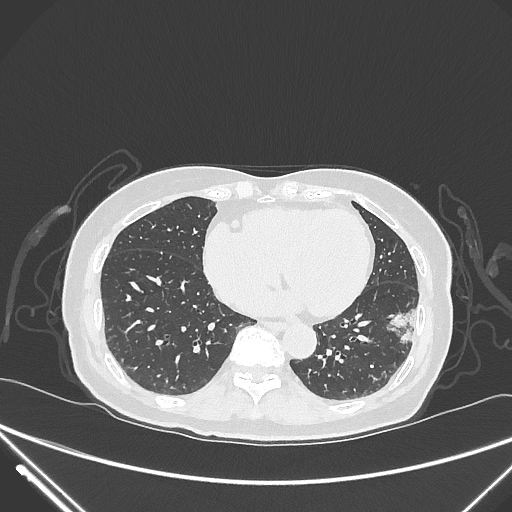
Chest CT, one axial slice. Slice 109 of 310 in the series (ordered by position). Lung window (W 1500 / L -600 HU). 1 mm slice thickness. 512 × 512 image matrix, field of view 377 × 377 mm. Patient: female, 82 years. From the clinical record (not read from this slice): clinical TNM (as recorded): T1c N0 M0.
Annotated regions visible in this slice (bounding box drawn by a radiologist):
- lung tumour (recorded histology: adenocarcinoma): bounding box (x1, y1, x2, y2) in pixels: (378, 294, 427, 347)